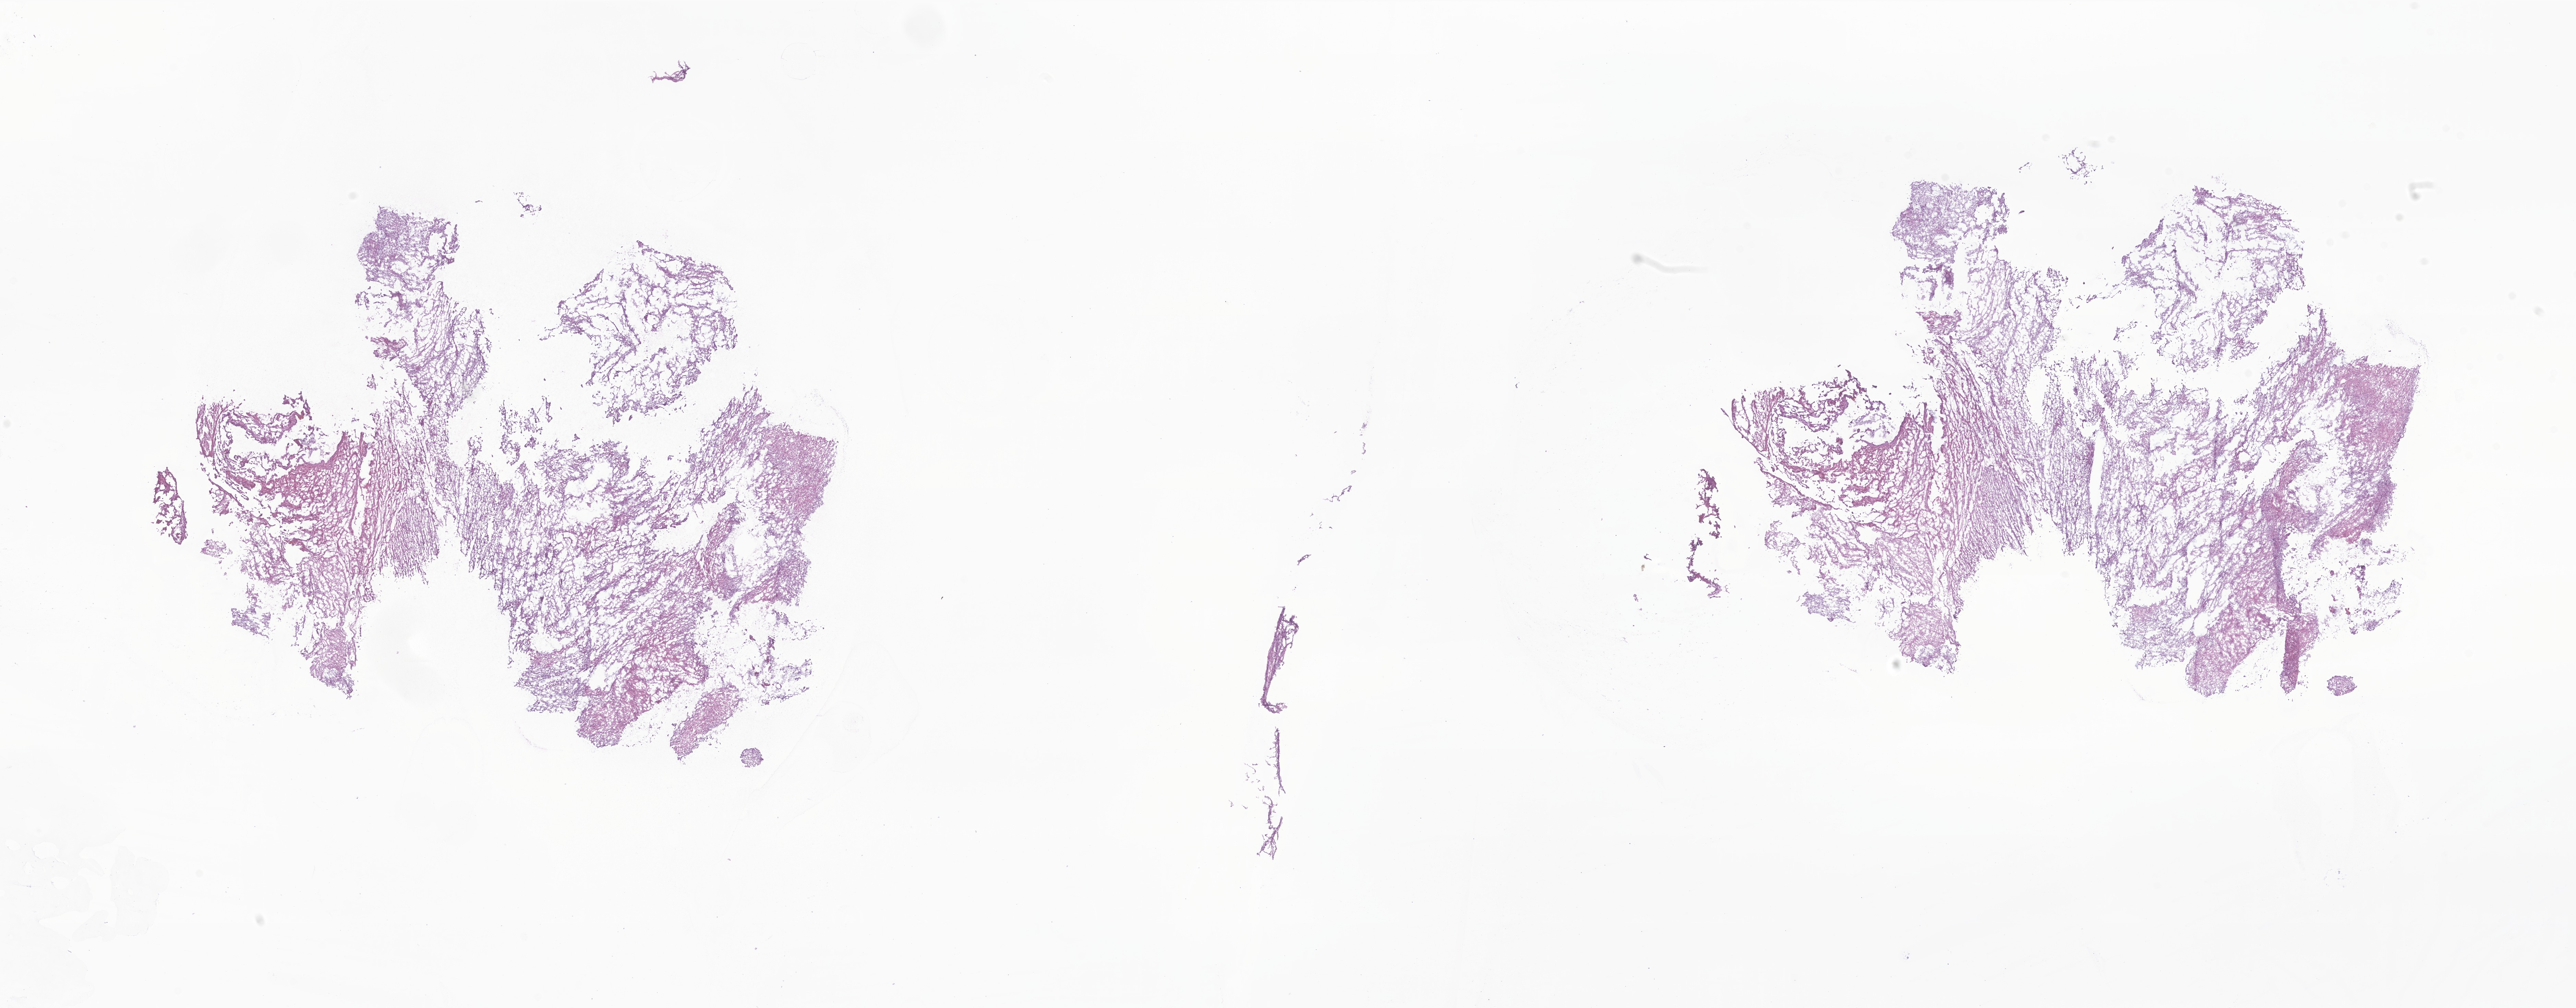
Whole-slide image, haematoxylin and eosin stain of tumor tissue from the brain — low-resolution overview of the scanned area, about 31.7 x 12.4 mm, frozen section. Patient female; age 46 months.
• diagnosis: Pilocytic astrocytoma